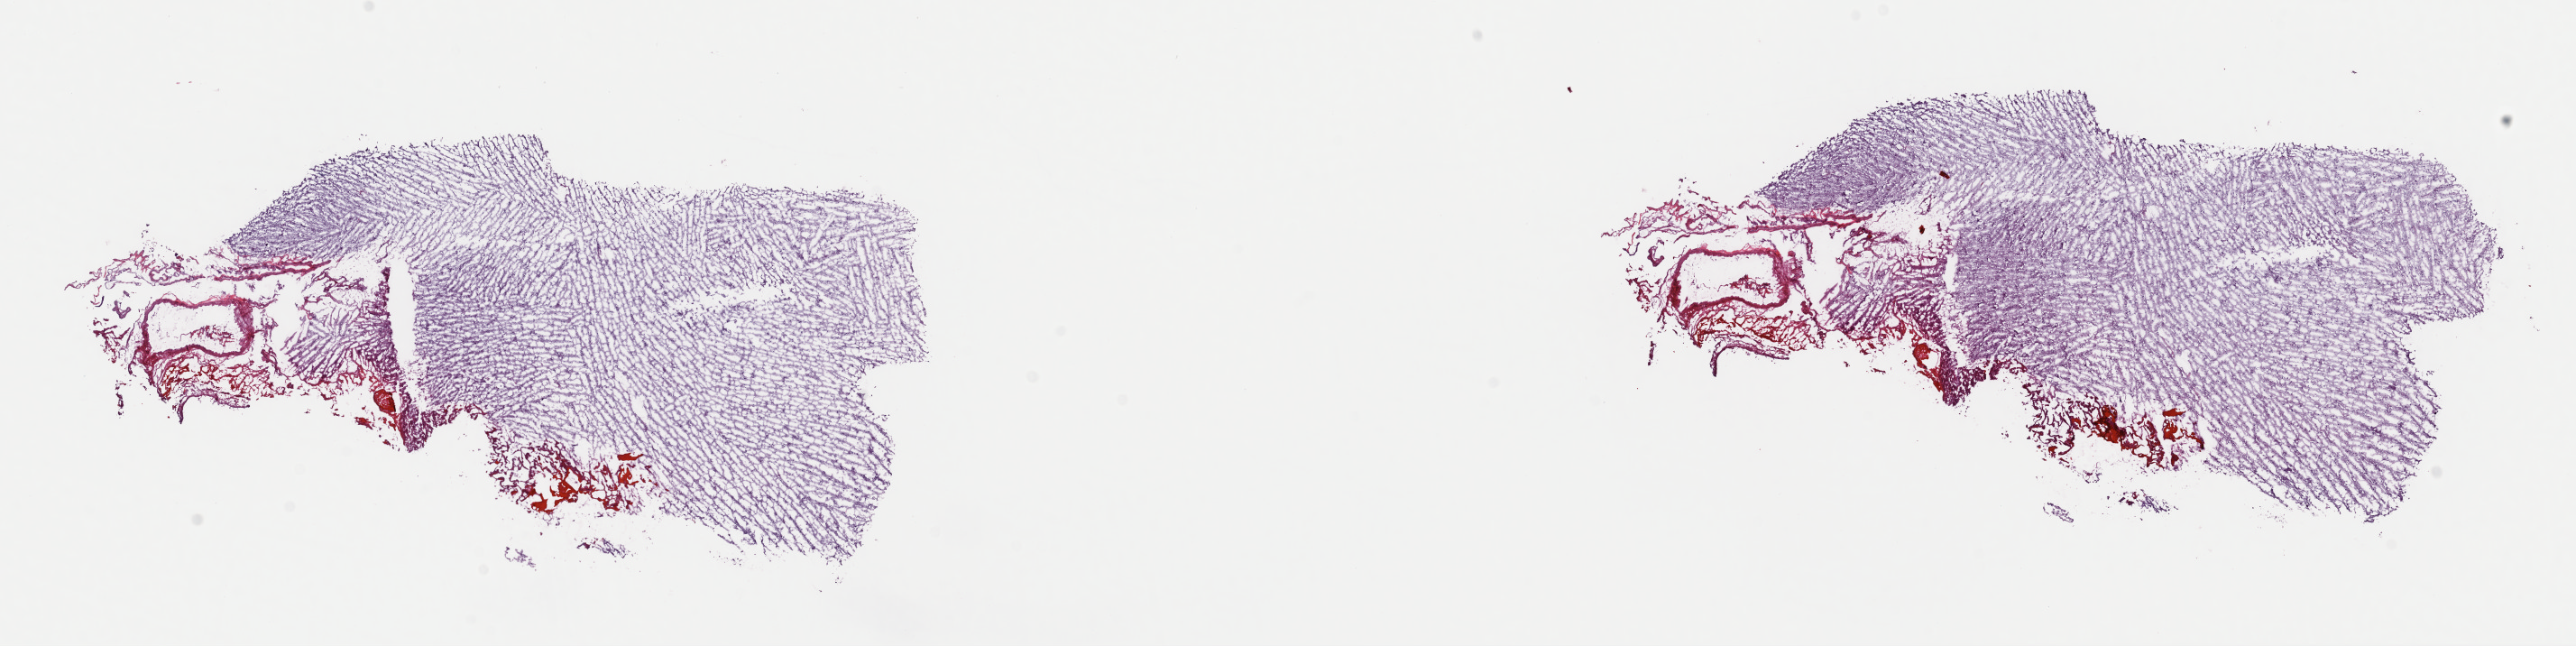
Whole-slide histology image, H&E-stained — whole scanned area (about 22.6 x 5.7 mm) shown as a low-resolution overview, frozen section from the top of the tissue portion, brain, primary tumour sample. Female, age 36 years at initial diagnosis. Histologic grade: G2 (moderately differentiated). Composition of this section per pathologist review: tumour cells 30%, tumour nuclei 70%, normal cells 10%, stromal cells 60%, necrosis 0%. Infiltration values recorded for this section: lymphocyte infiltration 0%, monocyte infiltration 0%, neutrophil infiltration 0%.
Histologic diagnosis: Astrocytoma, NOS (cerebrum).